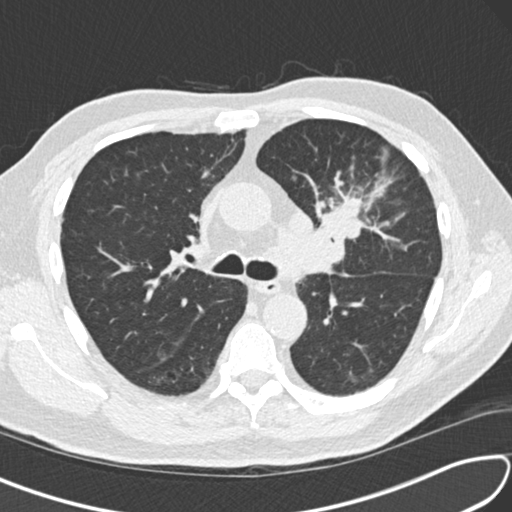
Low-dose screening chest CT, one axial slice. Position 100 of 156 along the scan axis. Reconstruction kernel B30f. Lung window (W 1500 / L -600 HU). 2 mm slice thickness. 512 × 512 image matrix, field of view 340 × 340 mm.
Structures marked on this image (expert manual segmentation):
- lesion 1 (tumor, upper lobe of left lung): bounding box [x1, y1, x2, y2] px = [320, 199, 361, 240]